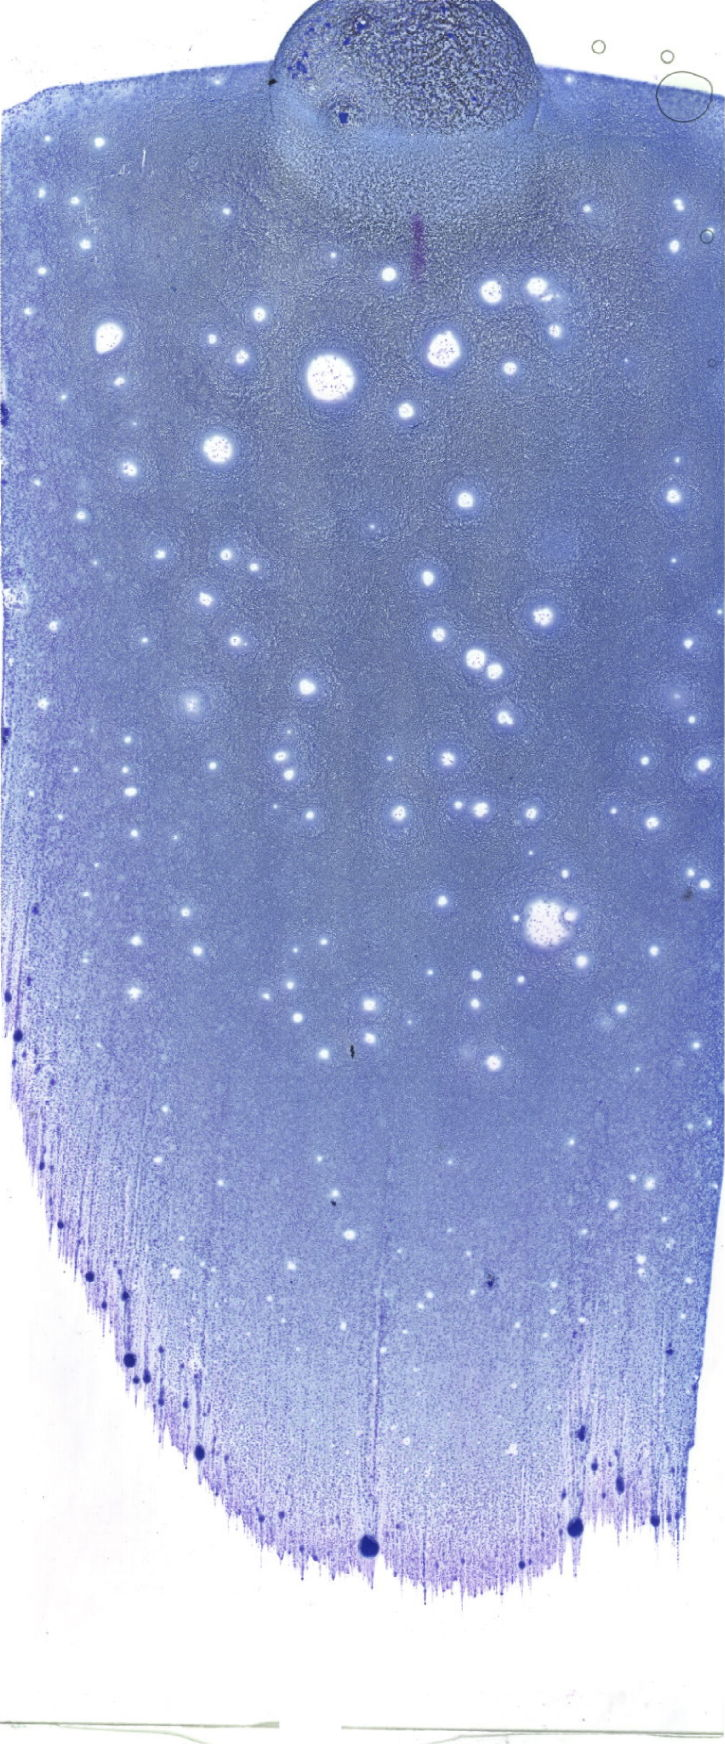
May-Grünwald-Giemsa (MGG)-stained marrow aspirate smear (whole slide) — shown as a low-resolution overview of the whole scanned area (about 20.6 x 49.4 mm). Male patient.
Diagnosis: Acute Myelomonocytic Leukemia with Abnormal Eosinophils.